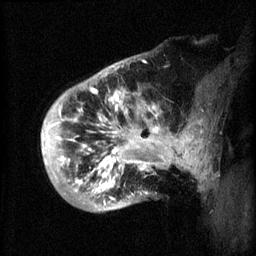
Breast MRI (dynamic contrast-enhanced), one sagittal slice; slice 11 of 60 in the series (ordered by position); 3 images stored at this slice position (order not interpretable as contrast timing); 1.5 T; TE 4.2 ms, TR 8.2 ms; 2 mm slice thickness; 256 × 256 image matrix, field of view 200 × 200 mm. Female patient, age 50 years.
Outlined on this slice (semi-automatic segmentation, software-assisted and operator-edited):
- analysis volume of interest (the breast-tissue region the enhancement analysis was run in; not a lesion): bounding box <44,72,173,213> (left, top, right, bottom; pixels)
- tumour enhancement mask (voxels above the 70 % enhancement threshold inside the analysis volume of interest): <44,88,173,205>